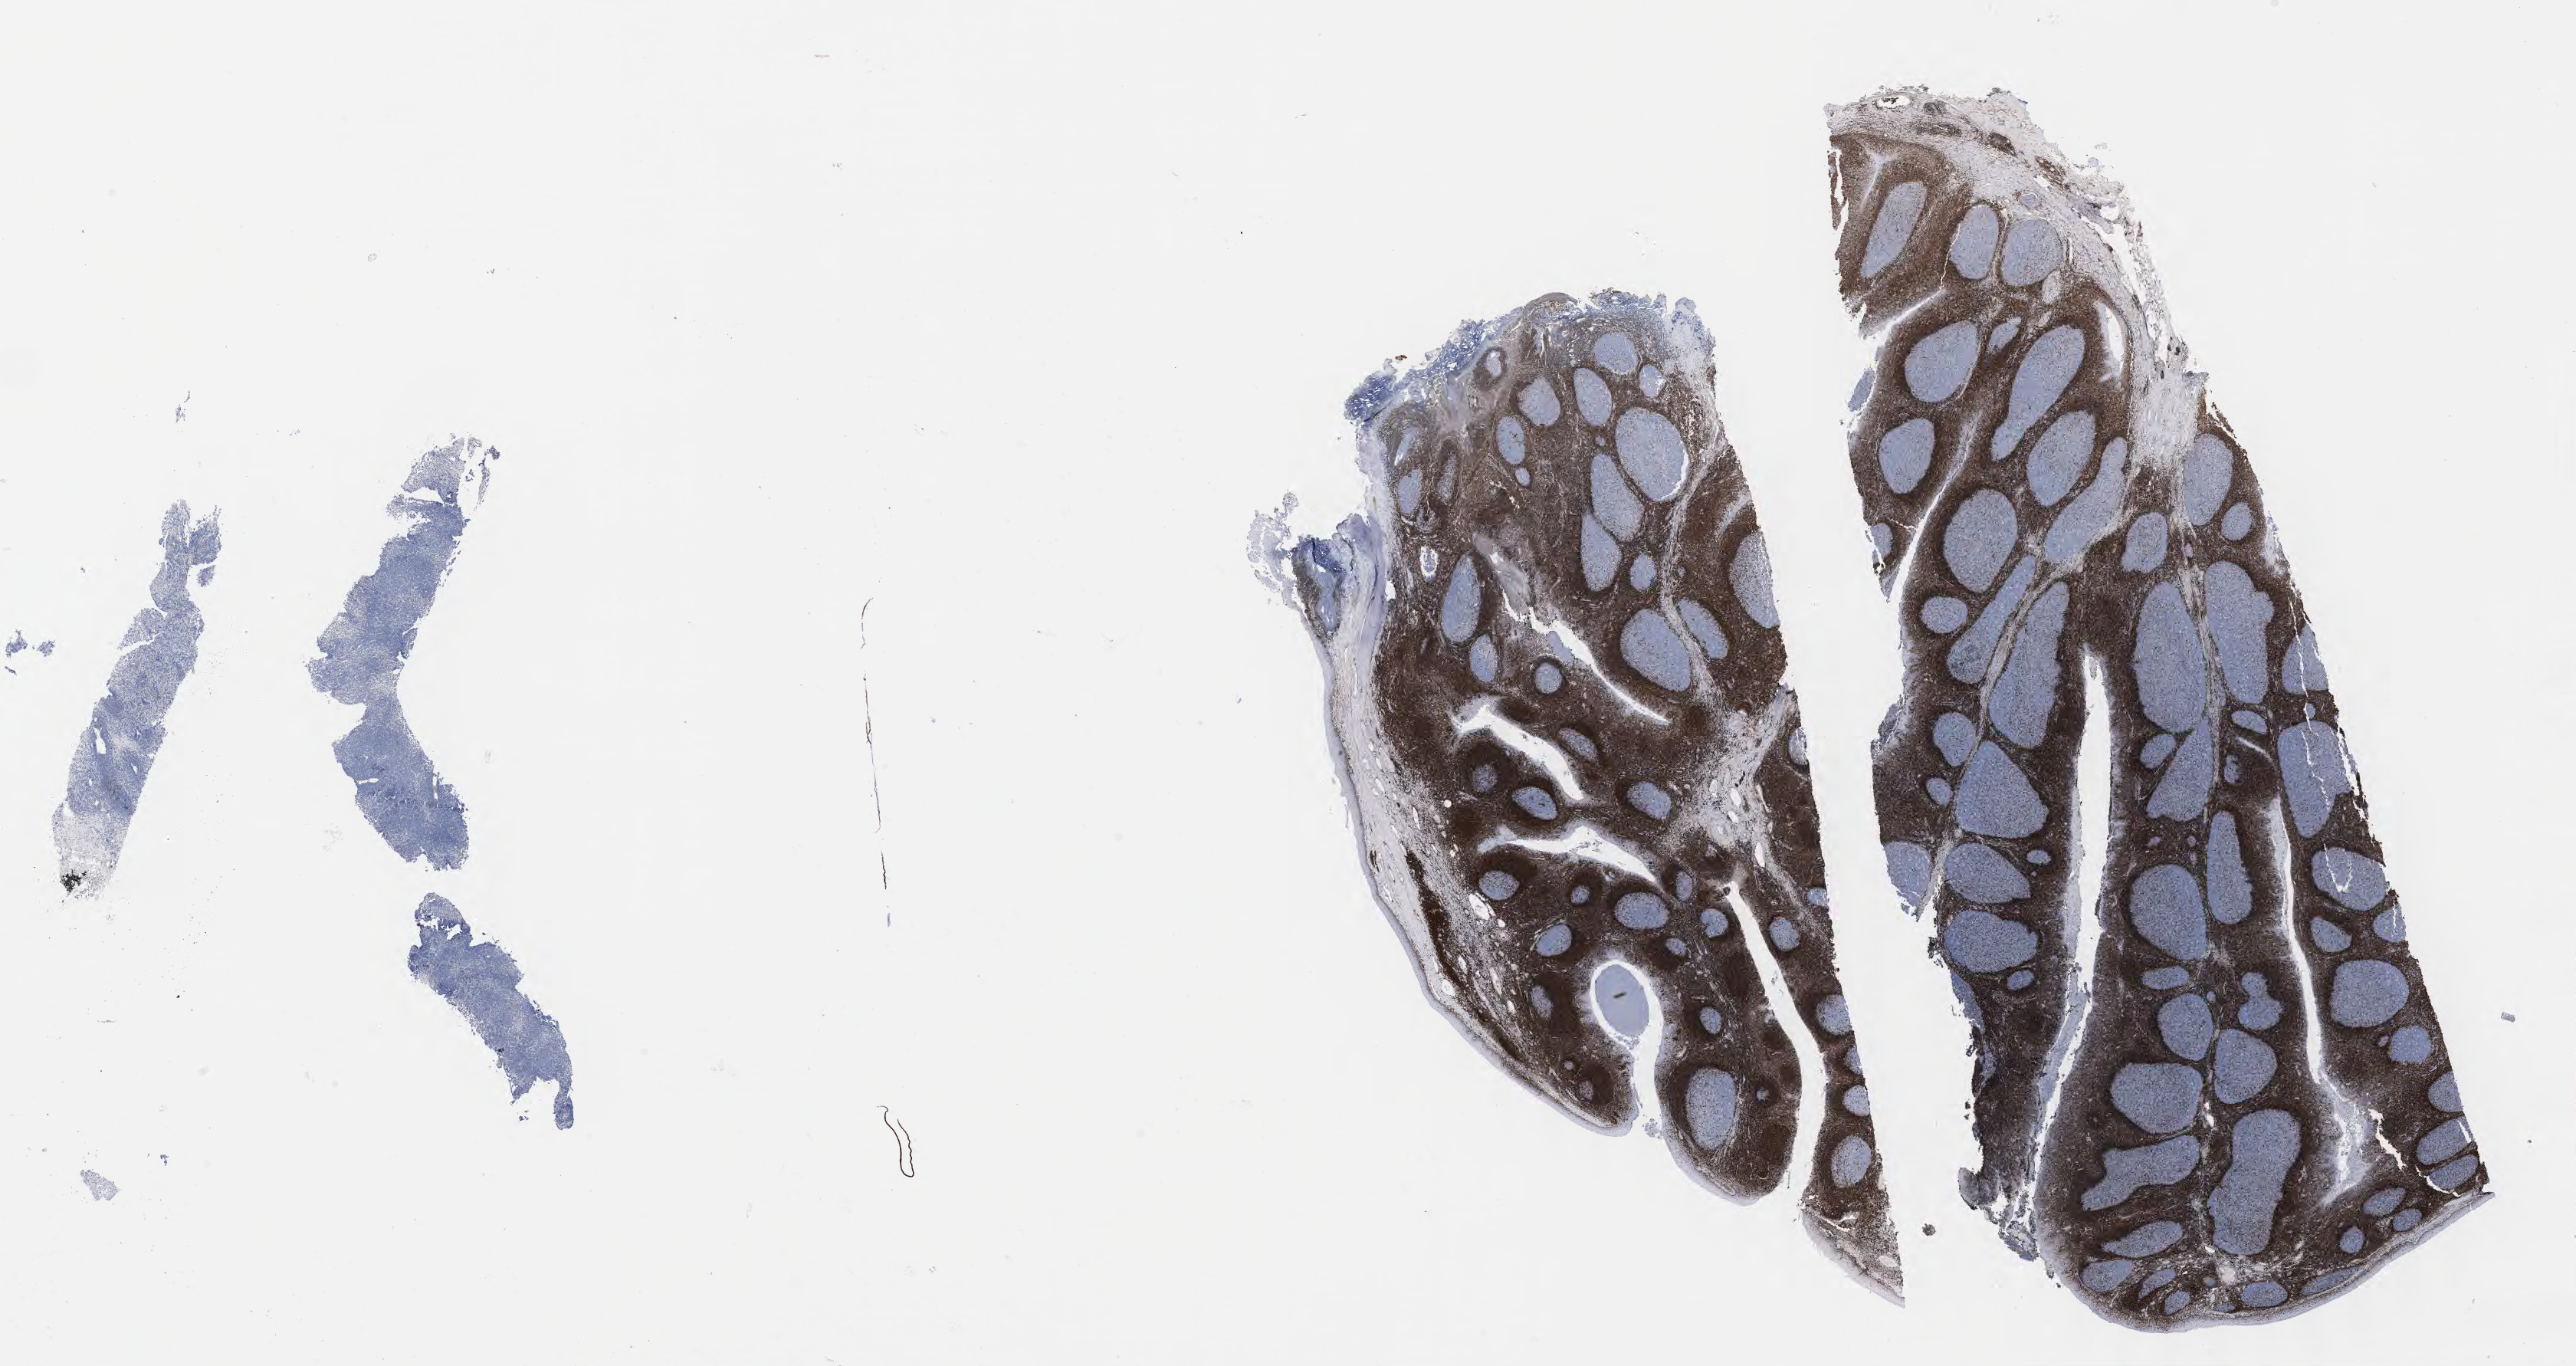
Immunohistochemistry (IHC) whole-slide image stained for BCL2, a low-resolution overview of the entire scanned area, about 27.2 x 14.4 mm, specimen: tumor tissue. Patient female; age 12 years.
• histologic diagnosis: Burkitt lymphoma, NOS